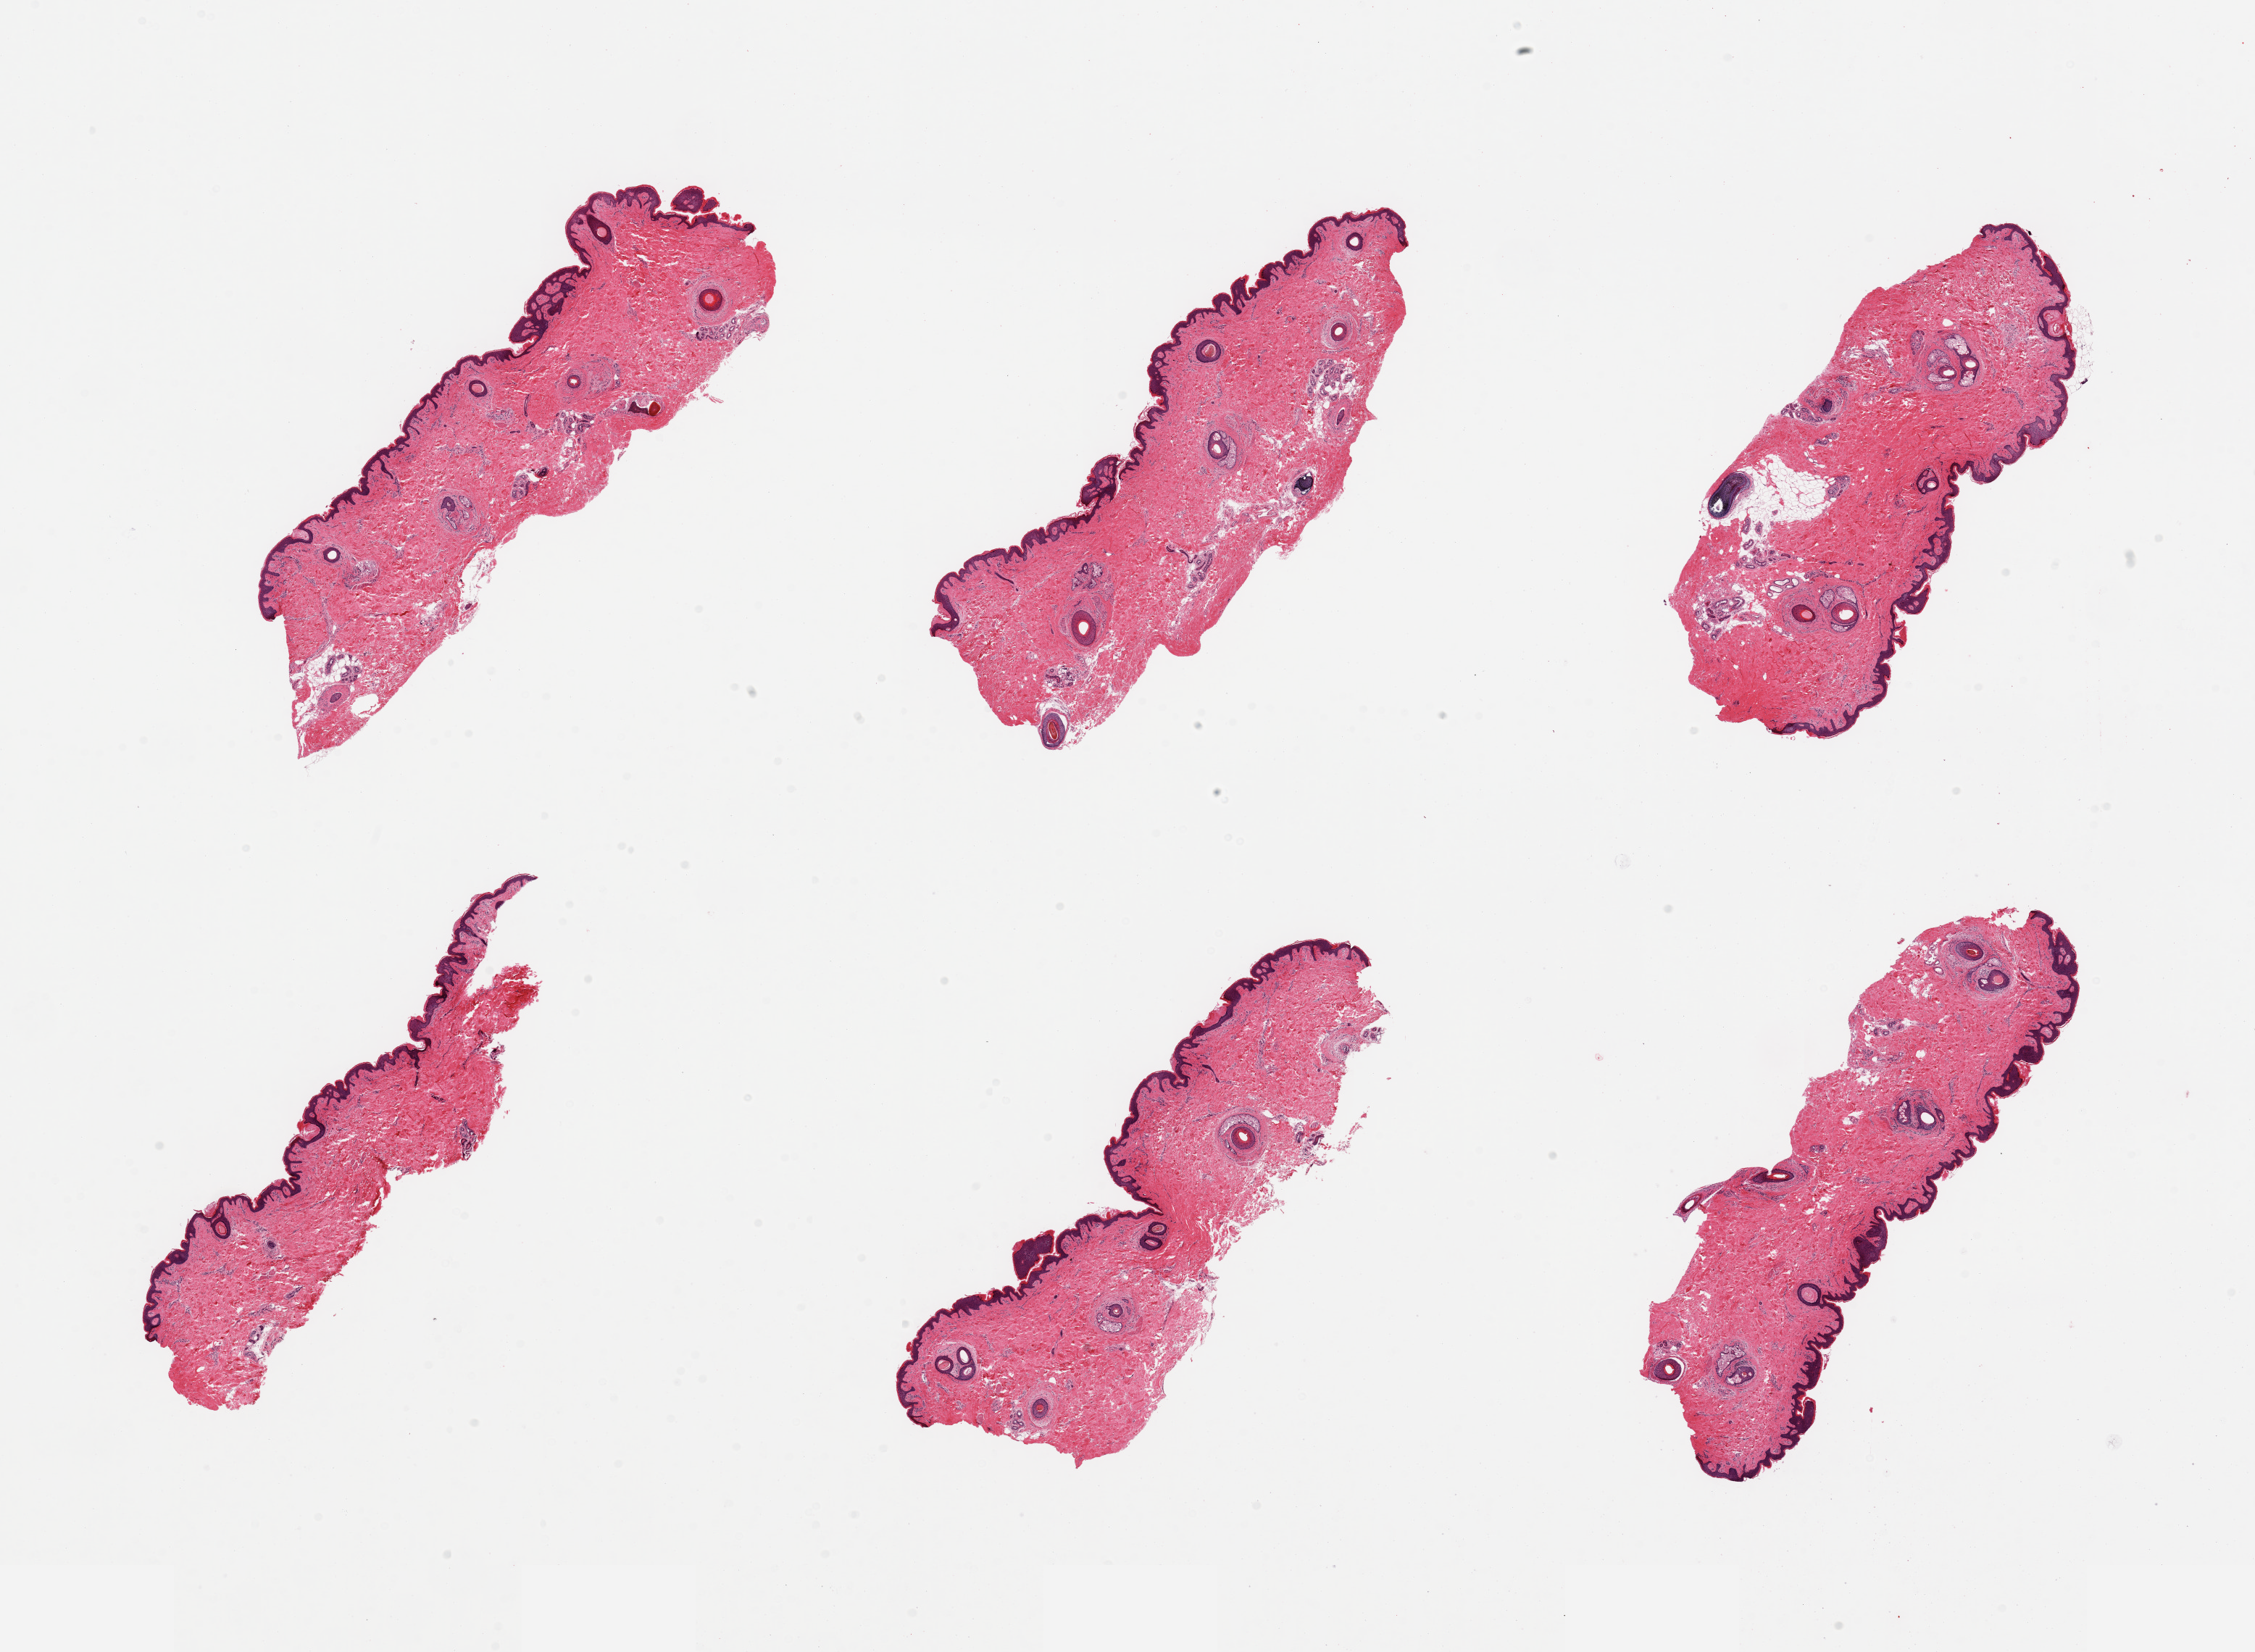
Haematoxylin and eosin whole-slide image, low-resolution overview of the scanned area, about 24.6 x 18.0 mm, PAXgene-fixed paraffin-embedded (PFPE) section, target tissue: skin of suprapubic region, tissue donor sample.
Review note (as recorded): 6 pieces; up to 6 hair follicles per piece; well trimmed.